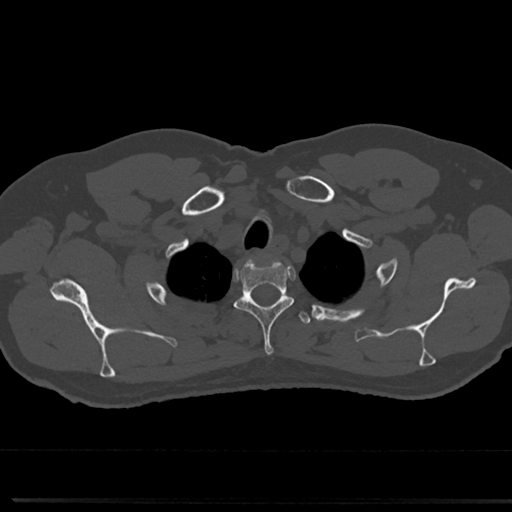
CT including the spine, one axial slice. Slice 630 of 817 in the series (ordered by position). Reconstruction kernel Br40s/3. 120 kVp. Bone window (W 1800 / L 400 HU). 0.5 mm slice thickness. 512 × 512 image matrix. Patient: male, 61 years. Case-level facts recorded for this patient, not image findings: primary cancer: prostate.
Structures marked on this image (semi-automatic segmentation, software-assisted and operator-edited):
- T1 vertebra: bounding box [x1, y1, x2, y2] px = [241, 298, 285, 302]
- T2 vertebra: [235, 253, 293, 357]
- T3 vertebra: [280, 298, 311, 327]